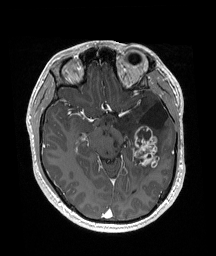
Brain MRI from a brain-tumour surgery series, one axial slice; position 104 of 192 along the scan axis; T1-weighted post-contrast; 216 × 256 image matrix, field of view 211 × 250 mm. Case-level facts recorded for this patient, not image findings: histopathology: Glioneuronal tumor; WHO grade: 2; tumour location: Left Superior Temporal Gyrus.
Outlined on this slice (manually delineated by an expert):
- previous resection cavity: bounding box <140,103,169,129> (left, top, right, bottom; pixels)
- tumour: <132,125,160,167>